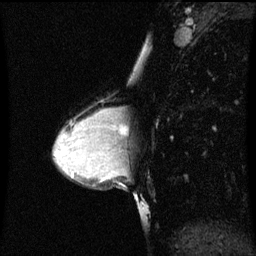
Breast MRI (dynamic contrast-enhanced), one sagittal slice. Slice 35 of 60 in the series (ordered by position). Dynamic contrast-enhanced series, image 2 of 3 at this slice position (ordered by acquisition). 1.5 T. TE 4.2 ms, TR 8.9 ms. 2 mm slice thickness. 256 × 256 image matrix, field of view 200 × 200 mm. Female patient, age 33 years. Case-level facts recorded for this patient, not image findings: setting: breast cancer imaged before/during neoadjuvant chemotherapy; receptor status: HER2-positive.
Structures marked on this image (semi-automatic segmentation, software-assisted and operator-edited):
- analysis volume of interest (the breast-tissue region the enhancement analysis was run in; not a lesion): bounding box (x1, y1, x2, y2) in pixels: (107, 108, 120, 147)
- tumour enhancement mask (voxels above the 70 % enhancement threshold inside the analysis volume of interest): (112, 110, 119, 139)